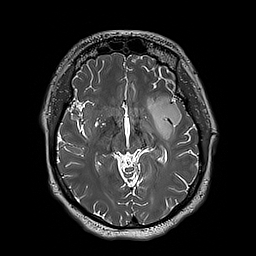
Brain MRI from a brain-tumour surgery series, one axial slice. Slice 110 of 192 in the series (ordered by position). 1 mm slice thickness. 256 × 256 image matrix, field of view 250 × 250 mm. Case-level facts recorded for this patient, not image findings: histopathology: Astrocytoma; WHO grade: 3; IDH mutation: yes.
Structures marked on this image (outlined manually by an expert reader):
- tumour: bounding box (x1, y1, x2, y2) in pixels: (148, 96, 182, 141)